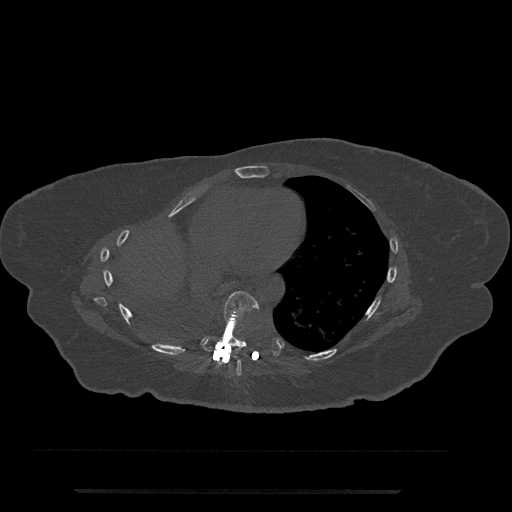
CT including the spine, one axial slice; slice 398 of 797 in the series (ordered by position); reconstruction kernel Br40s/3; 120 kVp; bone window (W 1800 / L 400 HU); 512 × 512 image matrix, field of view 440 × 440 mm. Patient: female, 51 years. From the clinical record (not read from this slice): primary cancer: neuro; vertebrae with lytic lesions (as recorded): T8.
Outlined on this slice (semi-automatic segmentation, software-assisted and operator-edited):
- T7 vertebra: bounding box <233,339,274,376> (left, top, right, bottom; pixels)
- T8 vertebra: <201,291,260,352>